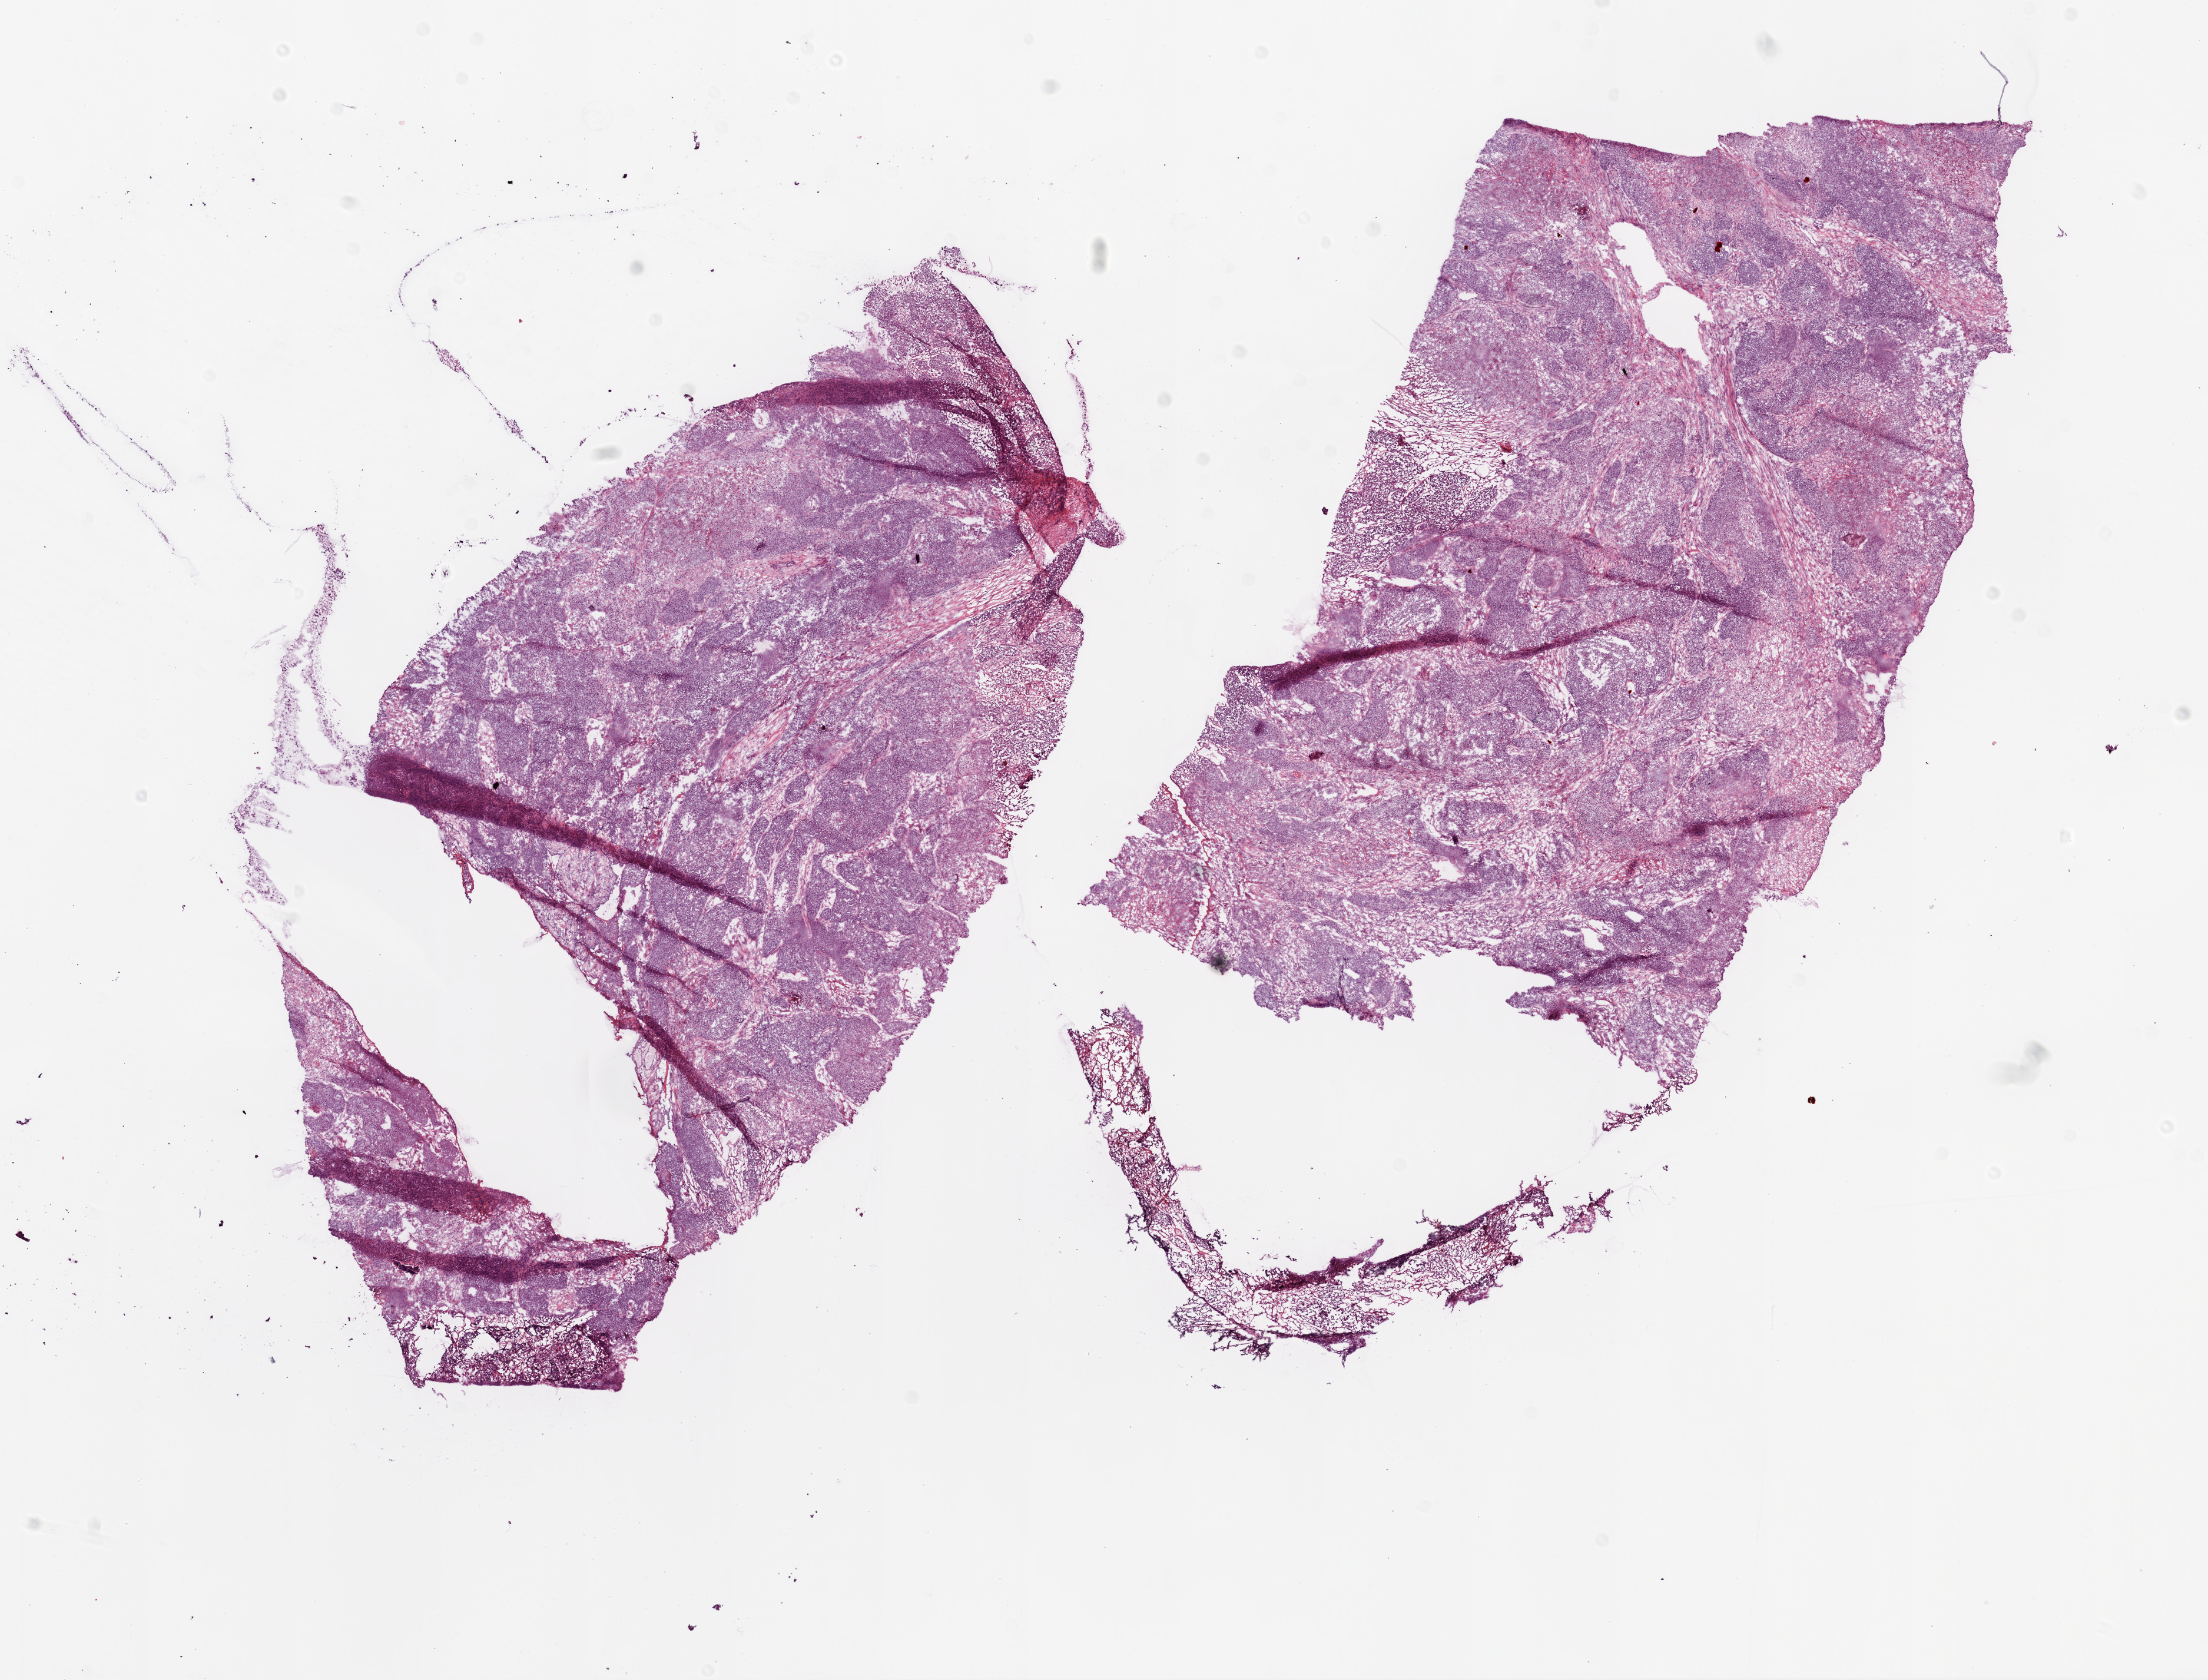
Digitized H&E-stained tissue section (whole slide) — a low-resolution overview of the entire scanned area, about 15.0 x 11.4 mm (acquisition: 20x scan). Frozen section. Ovary, primary tumour sample. Female patient; age at initial diagnosis 52 years. Composition of this section per pathologist review: tumour cells 85%, tumour nuclei 90%.
Diagnosis: Serous cystadenocarcinoma, NOS.